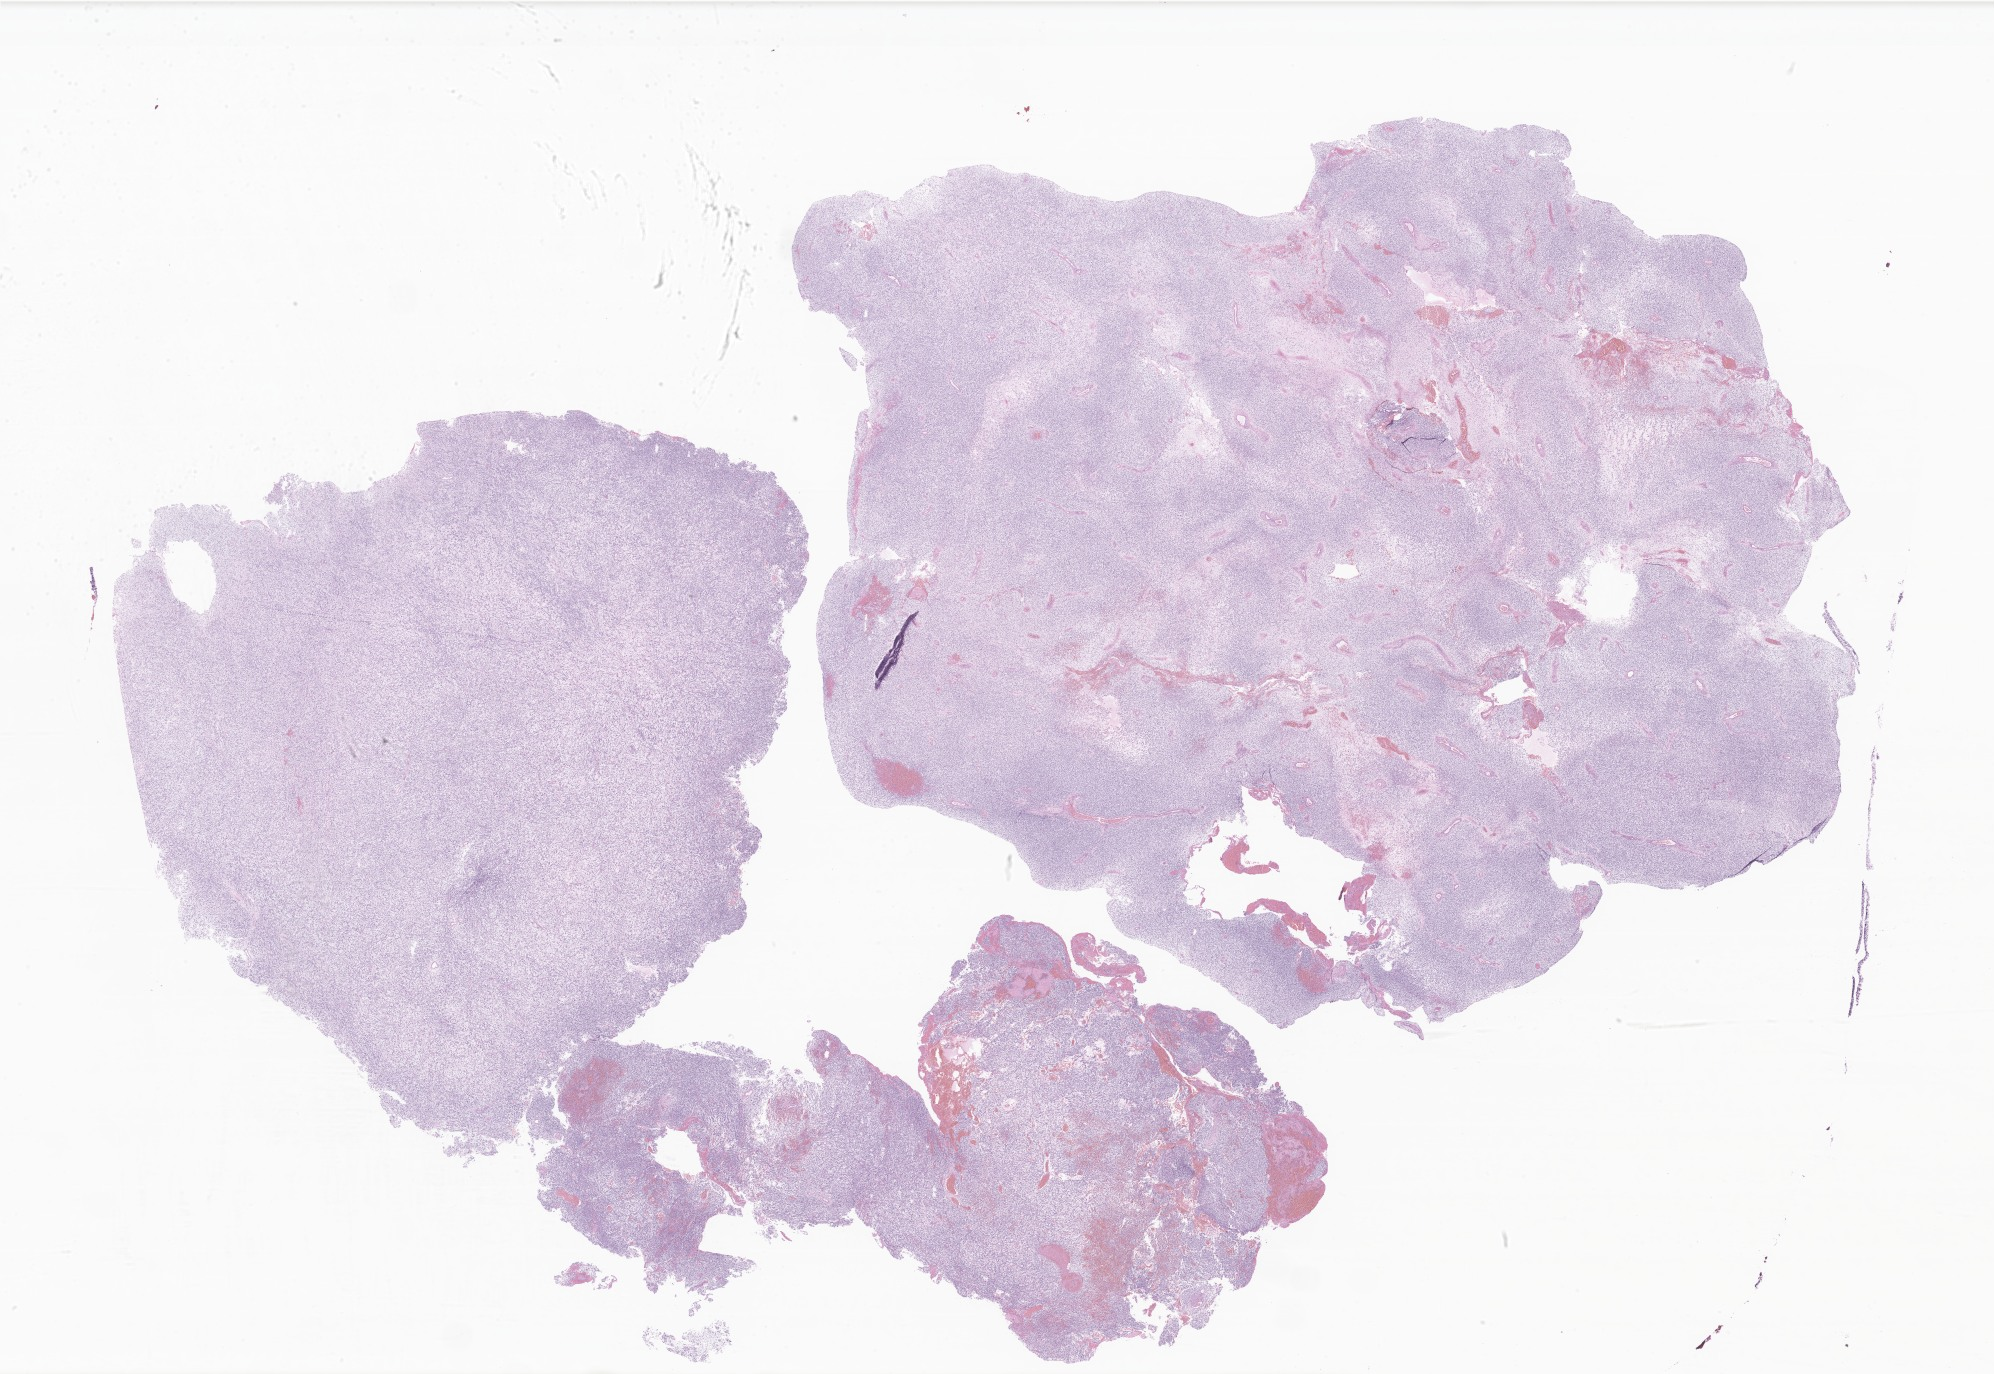
Whole-slide image, H&E stain of tumor tissue from the abdominal esophagus, a low-resolution overview of the entire scanned area, about 33.6 x 23.2 mm. Formalin-fixed, paraffin-embedded (FFPE) tissue. Patient: female, age 893 days.
* diagnosis: Rhabdomyosarcoma, NOS